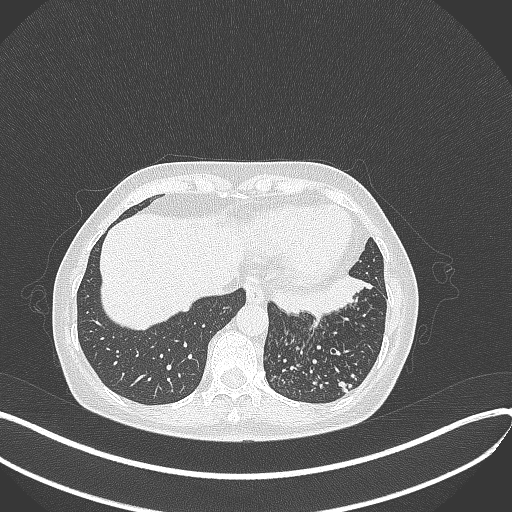
Chest CT, one axial slice; slice 97 of 429 in the series (ordered by position); reconstruction kernel B70f; 100 kVp; lung window (W 1500 / L -600 HU); 1 mm slice thickness; 512 × 512 image matrix, field of view 400 × 400 mm. Female patient, age 63 years. From the clinical record (not read from this slice): clinical TNM (as recorded): T1b N0 M0.
Structures marked on this image (bounding box drawn by a radiologist):
- lung tumour (recorded histology: adenocarcinoma): box from (x=269, y=270) to (x=374, y=320) px